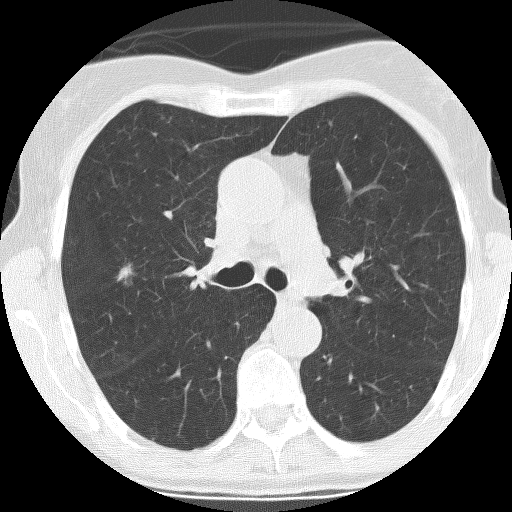
Low-dose screening chest CT, one axial slice; position 170 of 261 along the scan axis; lung window (W 1500 / L -600 HU); 2.5 mm slice thickness; 512 × 512 image matrix, field of view 270 × 270 mm.
Structures marked on this image (manually delineated by an expert):
- lesion 1 (tumor, upper lobe of right lung): bounding box [x1, y1, x2, y2] px = [118, 263, 136, 286]